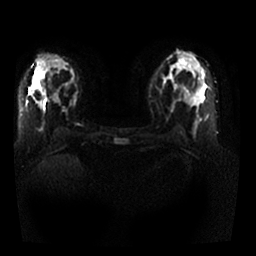
Breast MRI, one axial slice; slice 13 of 25 in the series (ordered by position); diffusion-weighted series; image 2 of 4 stored at this slice position (different b-values; order by instance number); 1.5 T; 4 mm slice thickness; 256 × 256 image matrix, field of view 330 × 330 mm. Female patient.
Outlined on this slice (outlined manually by an expert reader):
- tumour on diffusion-weighted imaging: bounding box [x1, y1, x2, y2] px = [30, 88, 33, 90]